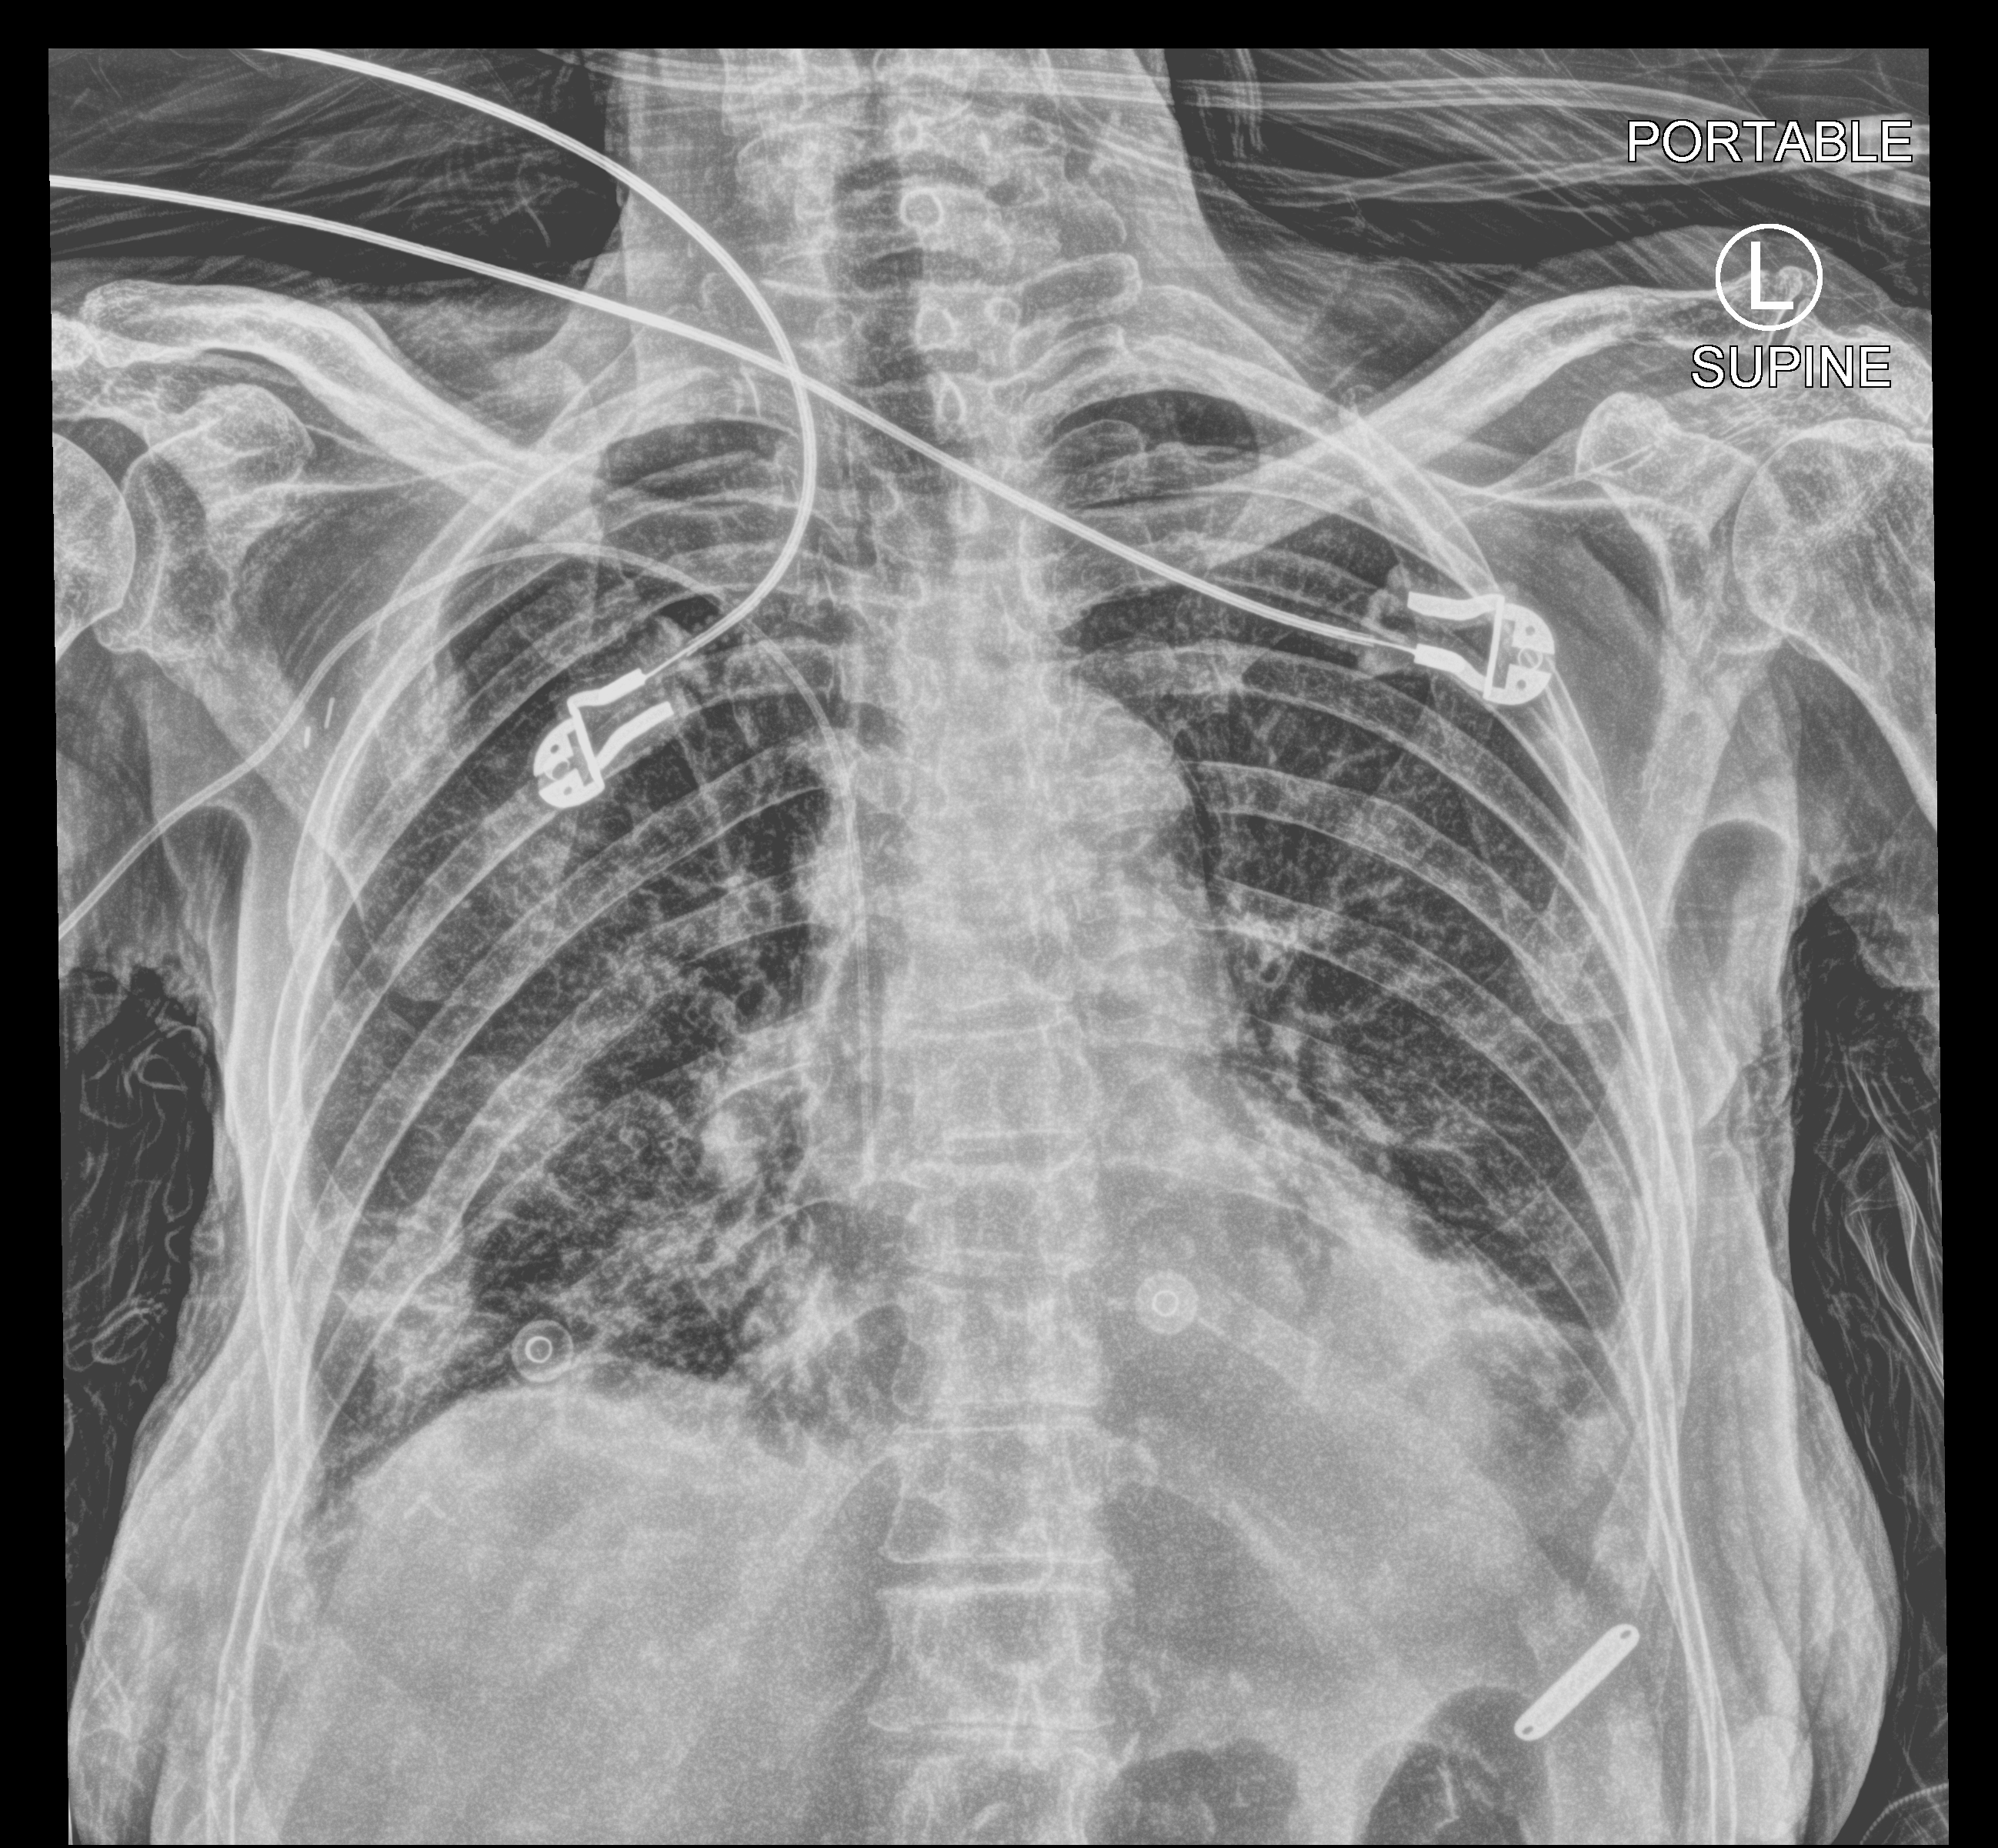
Portable chest radiograph. Patient hospitalised with COVID-19; female, aged 60–74 years.
From the hospital-stay record, not from the radiograph (when in the stay this image was taken is not recorded):
- length of hospital stay: 8 days
- admitted to intensive care during this hospital stay: no